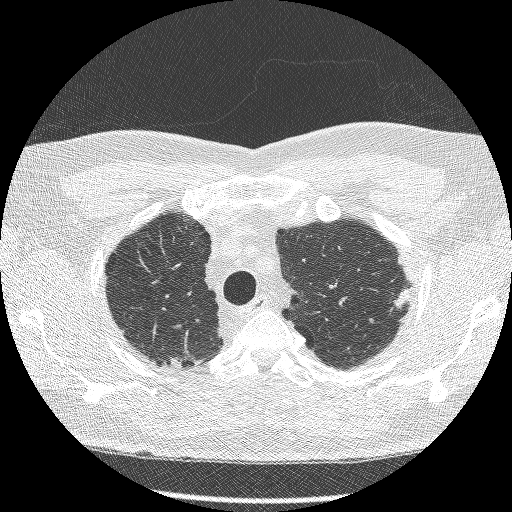
Axial slice from a low-dose chest CT screening exam; second annual screen; lung window (W 1500 / L -600 HU). Male, age 66 years at enrolment.
Lesion marked by an expert reader, bounding box <382,269,423,319> (left, top, right, bottom; pixels). Reader record for this screening exam (exam-level; its link to the box is not recorded): non-calcified nodule or mass ≥4 mm, right lower lobe, 40 × 19 mm, spiculated (stellate) margins, soft tissue attenuation, pre-existing on the prior screen: yes; interval growth: no. Note: the box lies in the patient's left hemithorax on this image, whereas the reader's record names the right lung; they may be different findings.